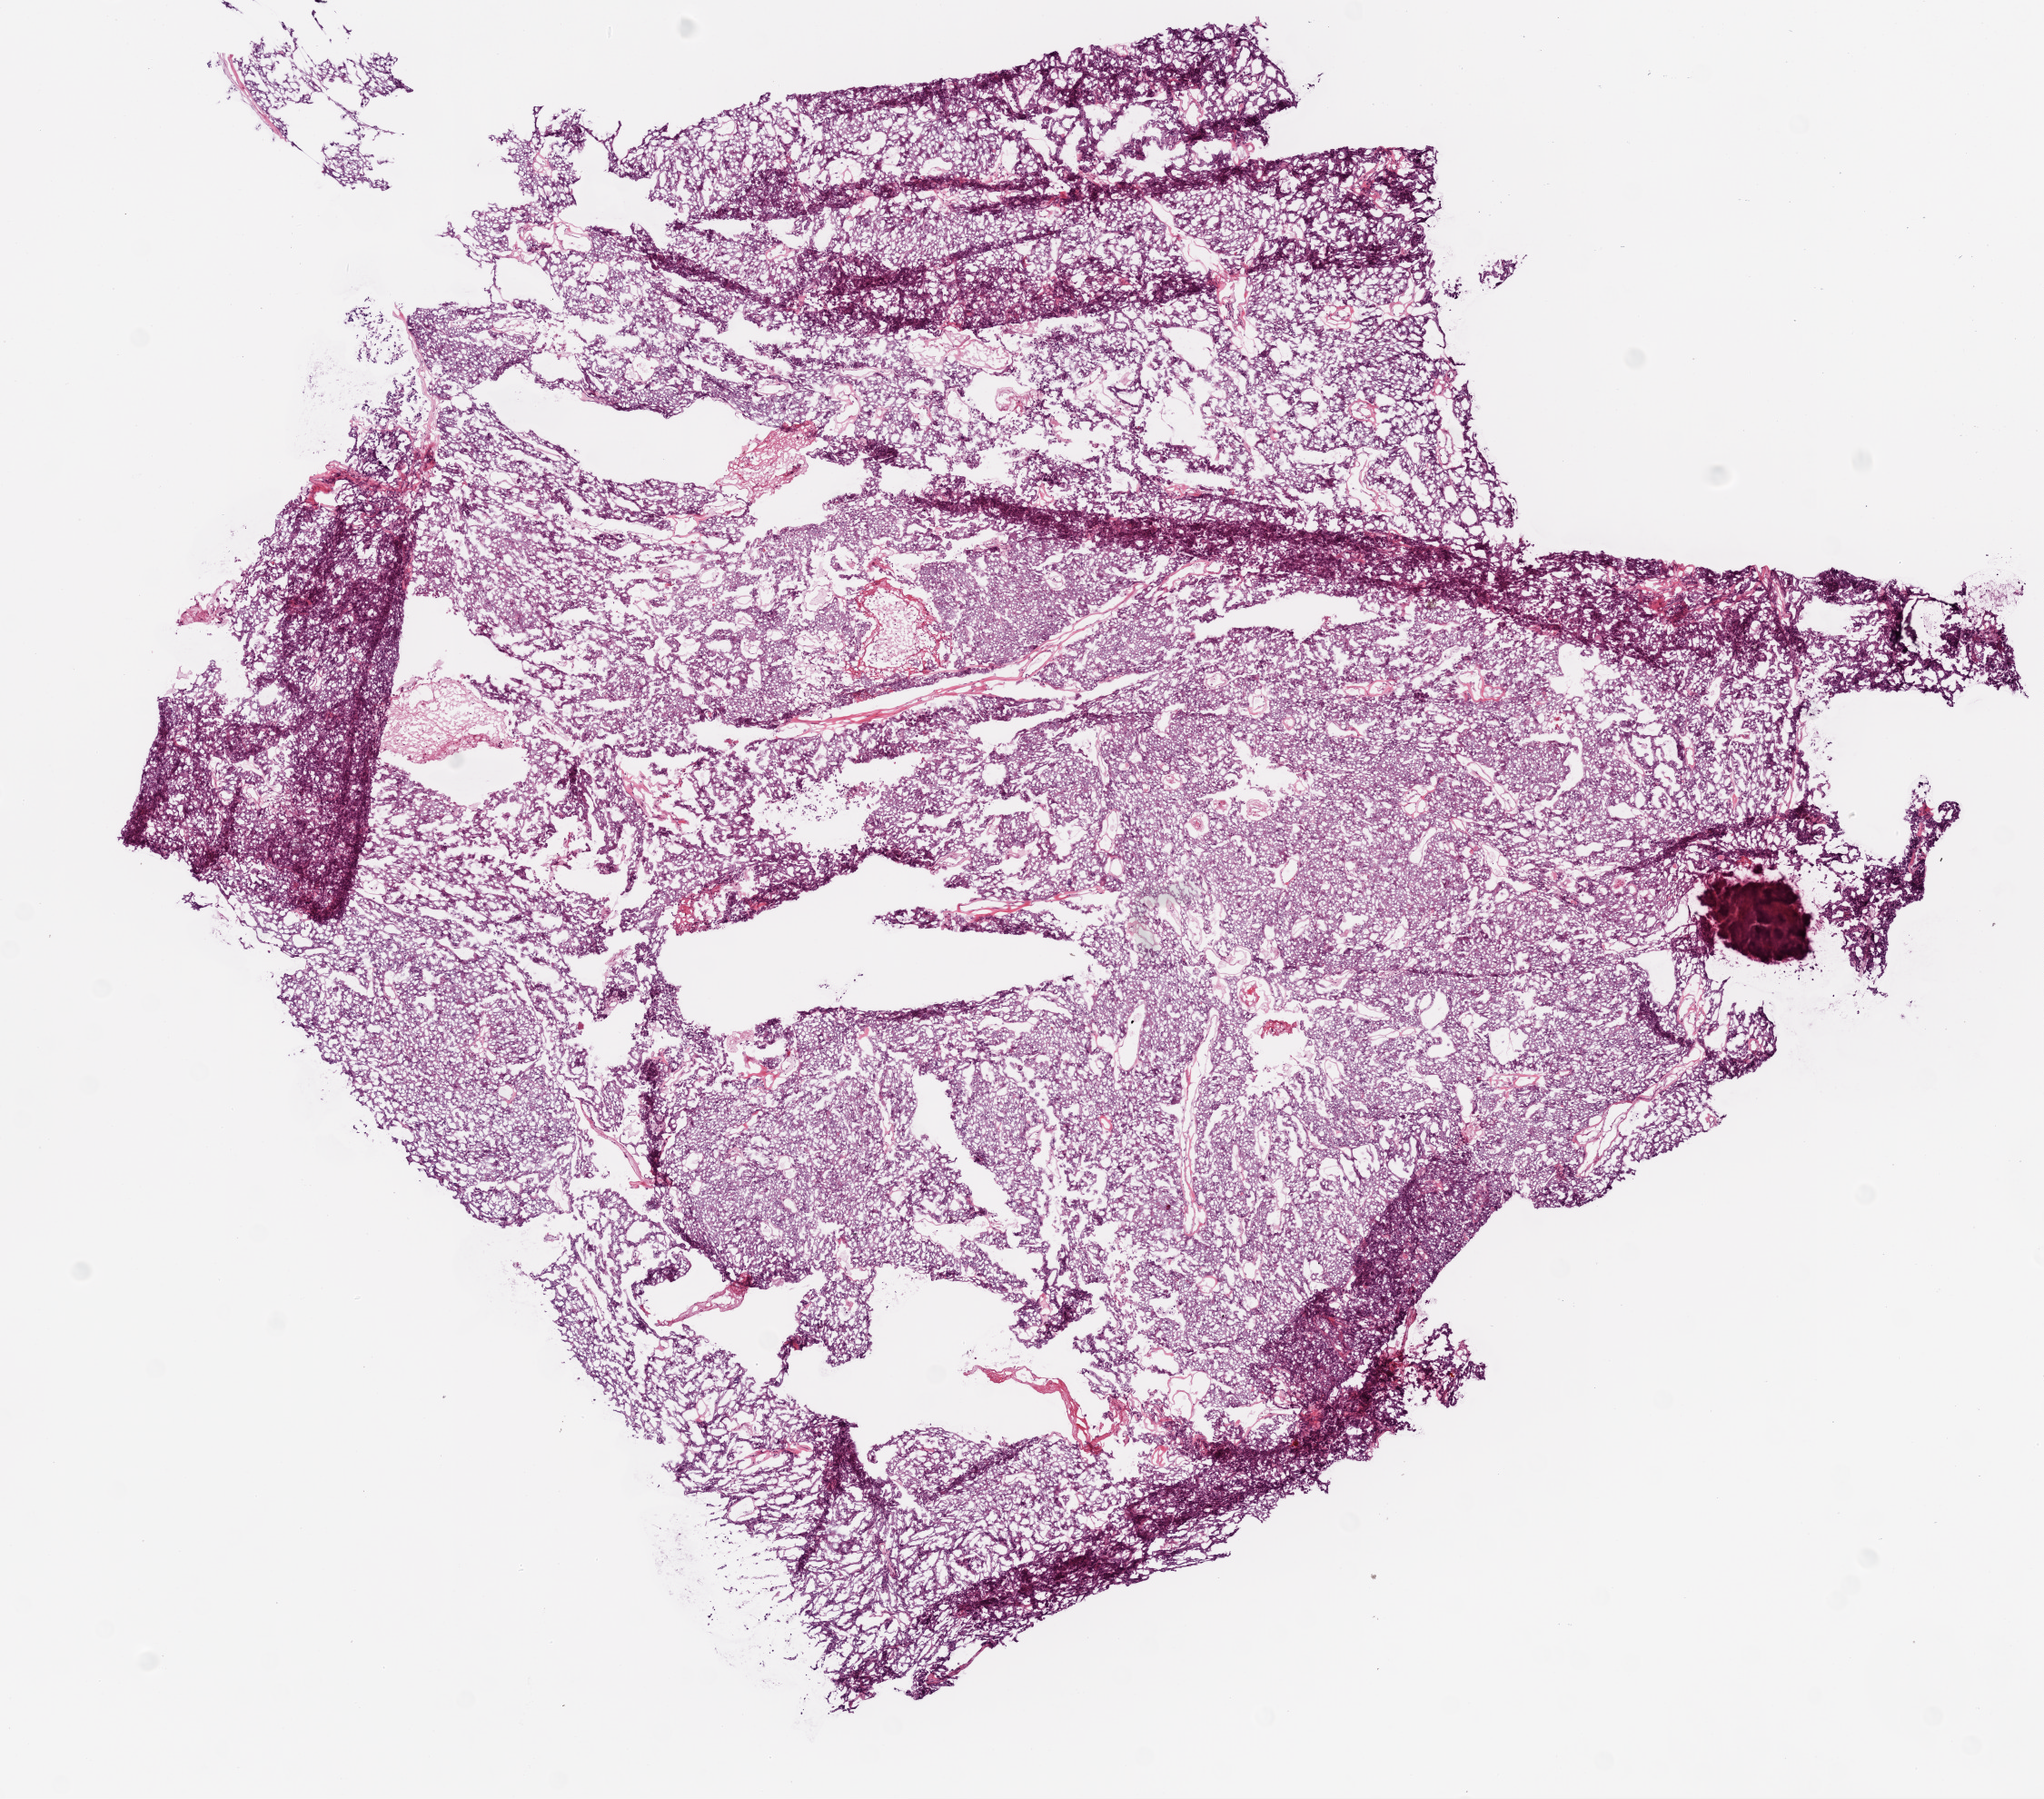
H&E-stained whole-slide image, whole scanned area (about 9.0 x 7.9 mm, acquisition: 20x scan) shown as a low-resolution overview. Frozen section. Sample: primary tumour, ovary. Female, age 60 years at initial diagnosis. Histologic grade: G3 (poorly differentiated). Composition of this section per pathologist review: tumour cells 98%, tumour nuclei 80%, normal cells 0%, stromal cells 2%, necrosis 0%.
* pathologic diagnosis: Serous cystadenocarcinoma, NOS
* FIGO stage: IIIC
* laterality: bilateral